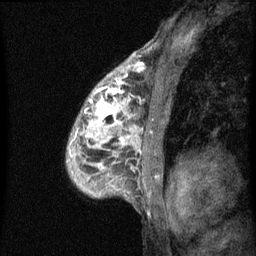
Breast MRI (dynamic contrast-enhanced), one sagittal slice; position 41 of 60 along the scan axis; dynamic contrast-enhanced series, image 2 of 3 at this slice position (ordered by acquisition); 1.5 T; TE 4.2 ms, TR 8 ms; 2 mm slice thickness; 256 × 256 image matrix, field of view 180 × 180 mm. Female patient, age 50 years.
Outlined on this slice (semi-automatically segmented with operator editing):
- analysis volume of interest (the breast-tissue region the enhancement analysis was run in; not a lesion): box from (x=66, y=64) to (x=141, y=187) px
- tumour enhancement mask (voxels above the 70 % enhancement threshold inside the analysis volume of interest): (x=95, y=64)–(x=141, y=167)